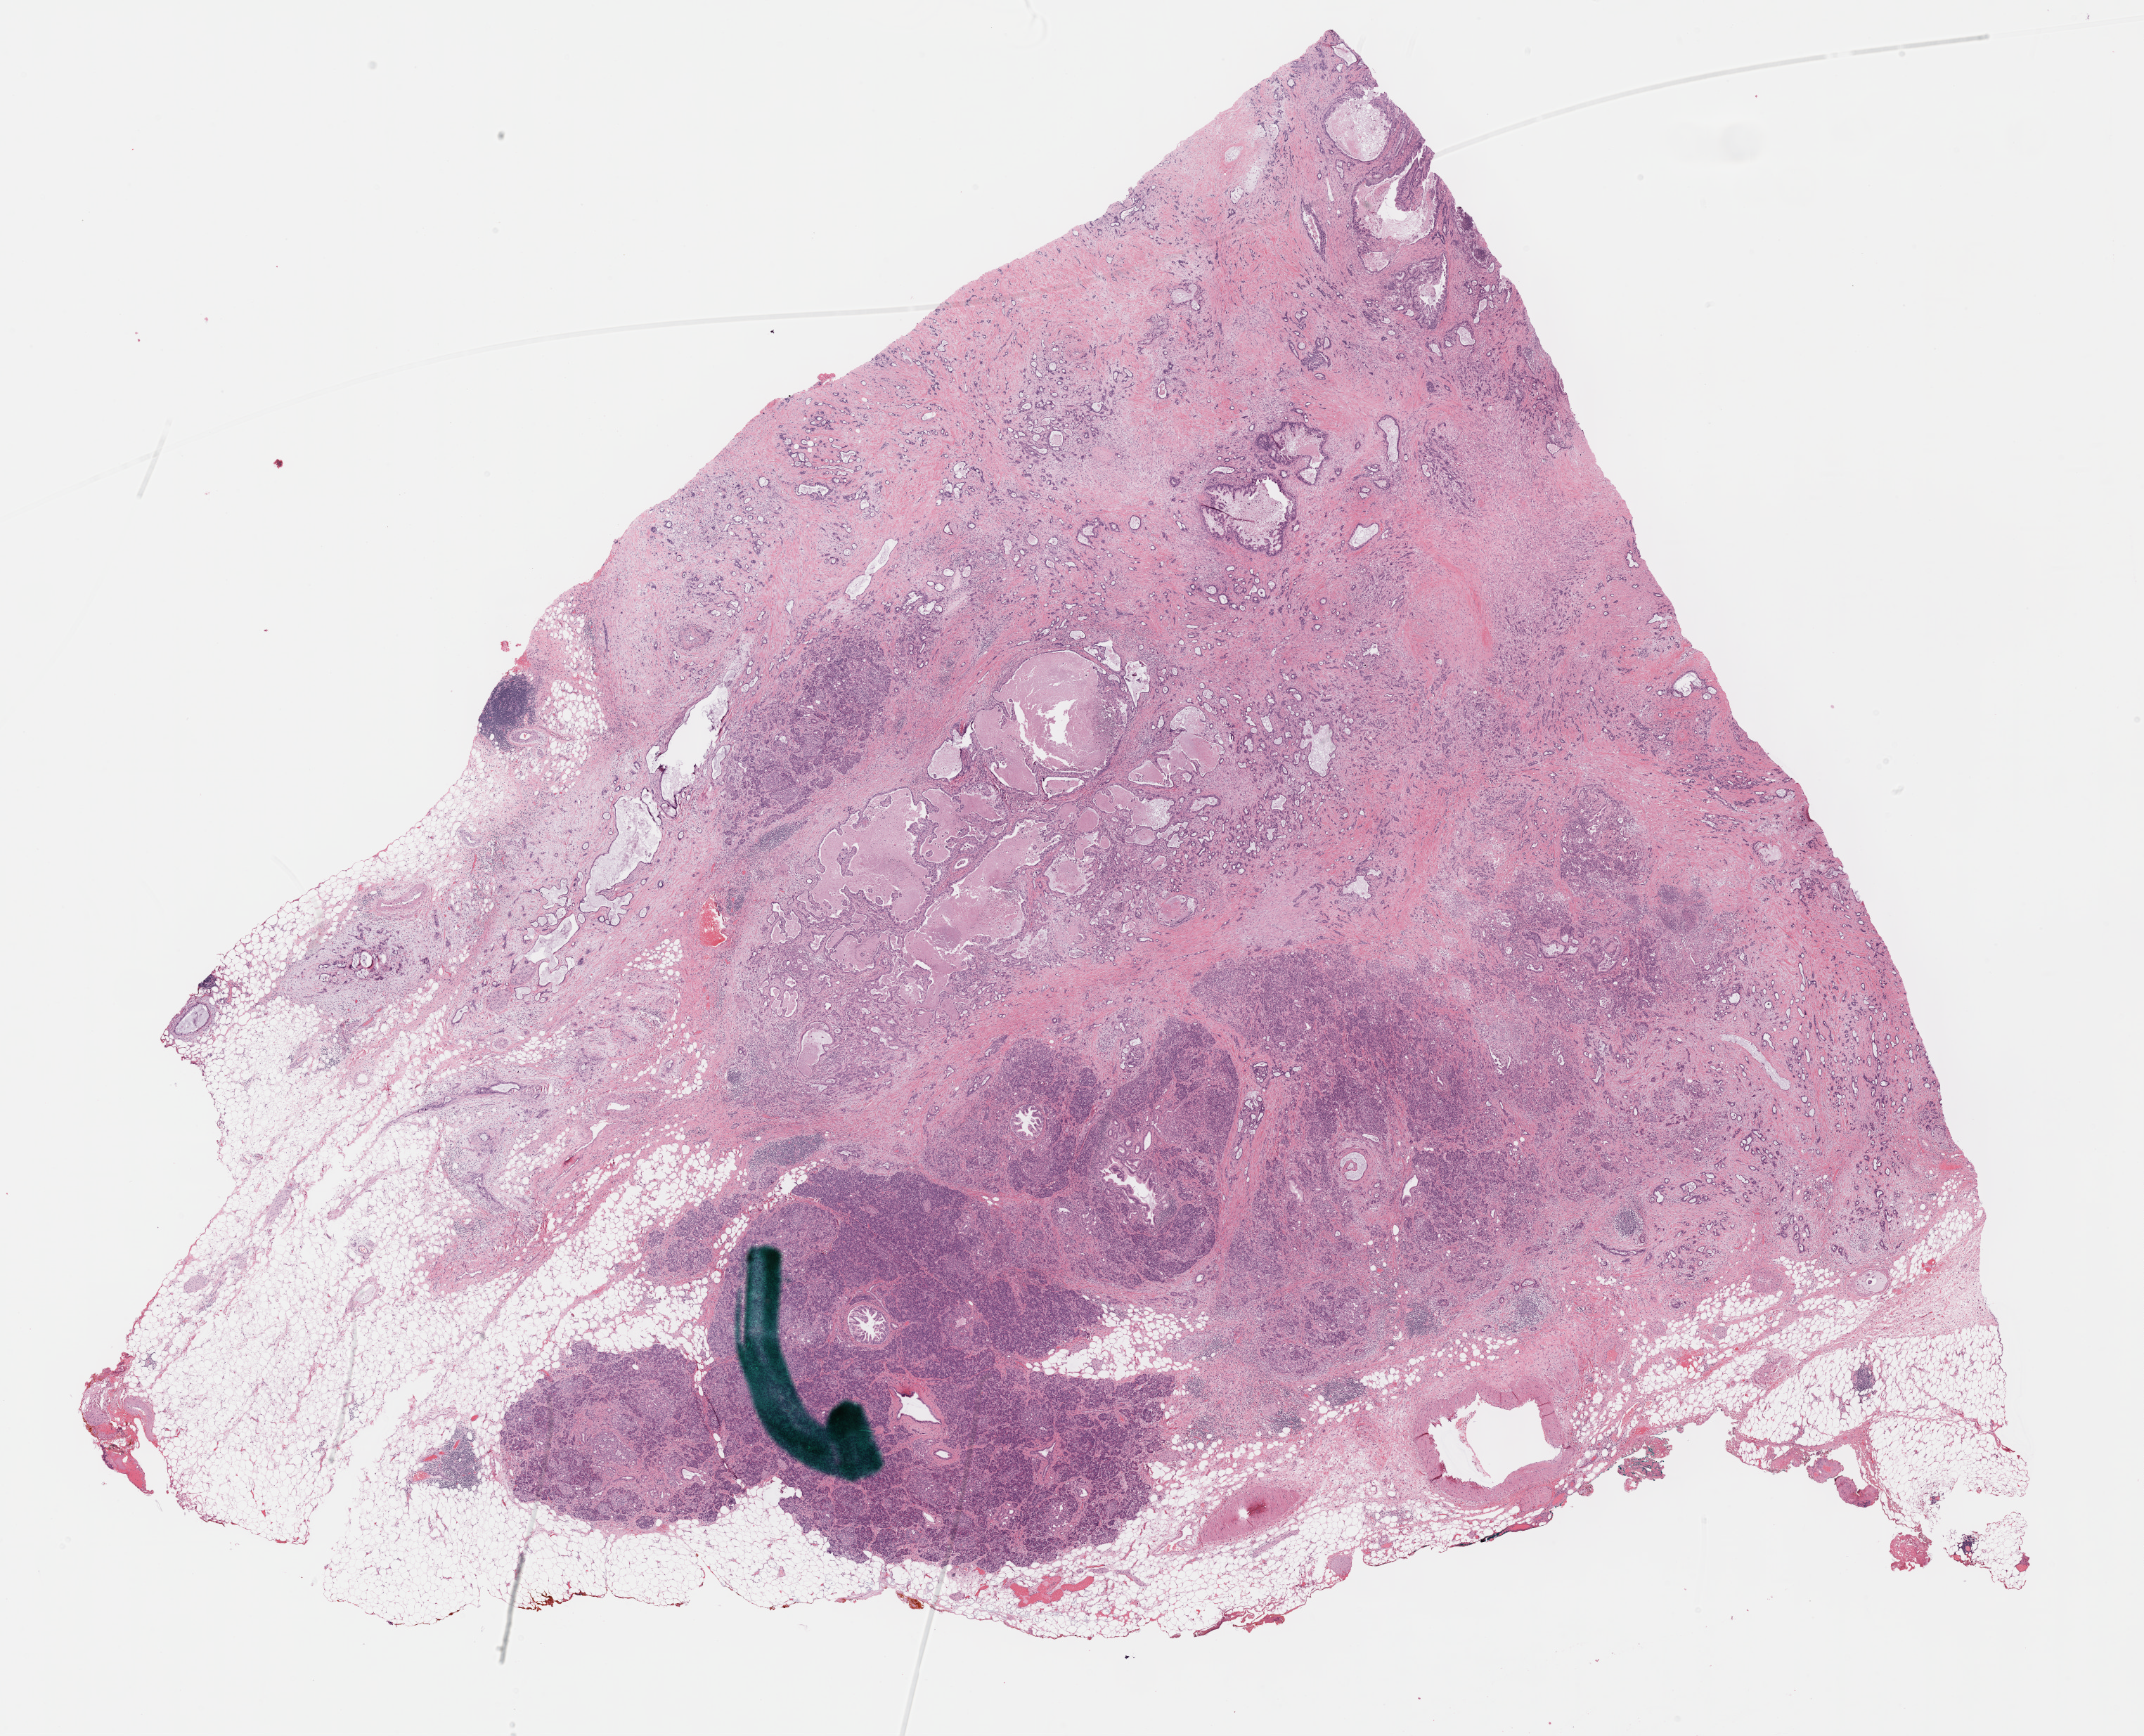
H&E whole-slide image, a low-resolution overview of the entire scanned area, about 24.7 x 20.0 mm (slide scanned at 40x), formalin-fixed paraffin-embedded (FFPE) diagnostic section, pancreas, primary tumour sample. Patient: male, age at initial diagnosis 65 years. Histologic grade: G3 (poorly differentiated).
- AJCC pathologic stage: IIB
- lymph nodes positive (case pathology): 16 of 19 examined
- diagnosis: Infiltrating duct carcinoma, NOS